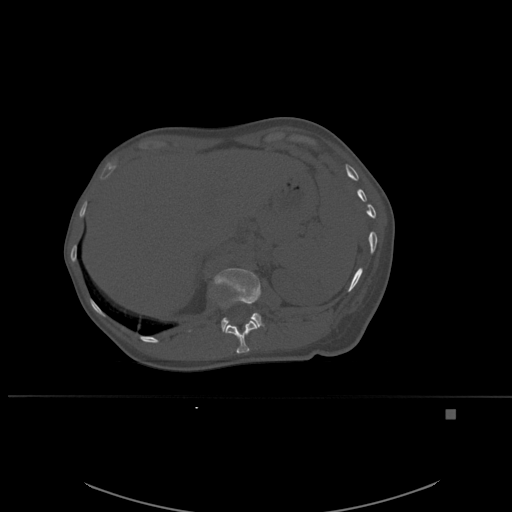
CT including the spine, one axial slice. Bone window (W 1800 / L 400 HU). 1.5 mm slice thickness. 512 × 512 image matrix, field of view 440 × 440 mm. Female patient, age 45 years. From the clinical record (not read from this slice): primary cancer: lung.
Structures marked on this image (semi-automatic segmentation, software-assisted and operator-edited):
- L1 vertebra: box from (x=214, y=268) to (x=264, y=332) px
- T12 vertebra: (x=213, y=279)–(x=258, y=354)